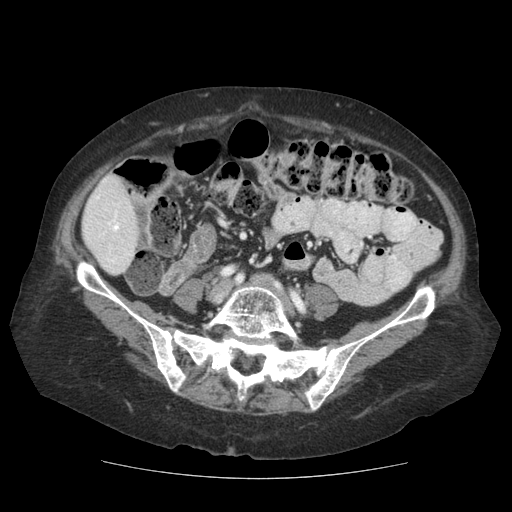
Contrast-enhanced abdominal CT (liver protocol), one axial slice; position 21 of 111 along the scan axis; reconstruction kernel STANDARD; 140 kVp; soft-tissue window (W 400 / L 40 HU); 512 × 512 image matrix, field of view 360 × 360 mm. Case-level facts recorded for this patient, not image findings: diagnosis: hepatocellular carcinoma (patient treated with transarterial chemoembolisation; whether this scan precedes or follows treatment is not stated here); TNM stage (as recorded): Stage-I; Child-Pugh class: A; tumour size: 7.3 cm.
Outlined on this slice (semi-automatically segmented with operator editing):
- liver parenchyma outside the tumour (the mass and vessels are separate outlines, so this box may not span the whole liver): bounding box (x1, y1, x2, y2) in pixels: (82, 174, 138, 274)
- liver vessels: (97, 197, 119, 231)